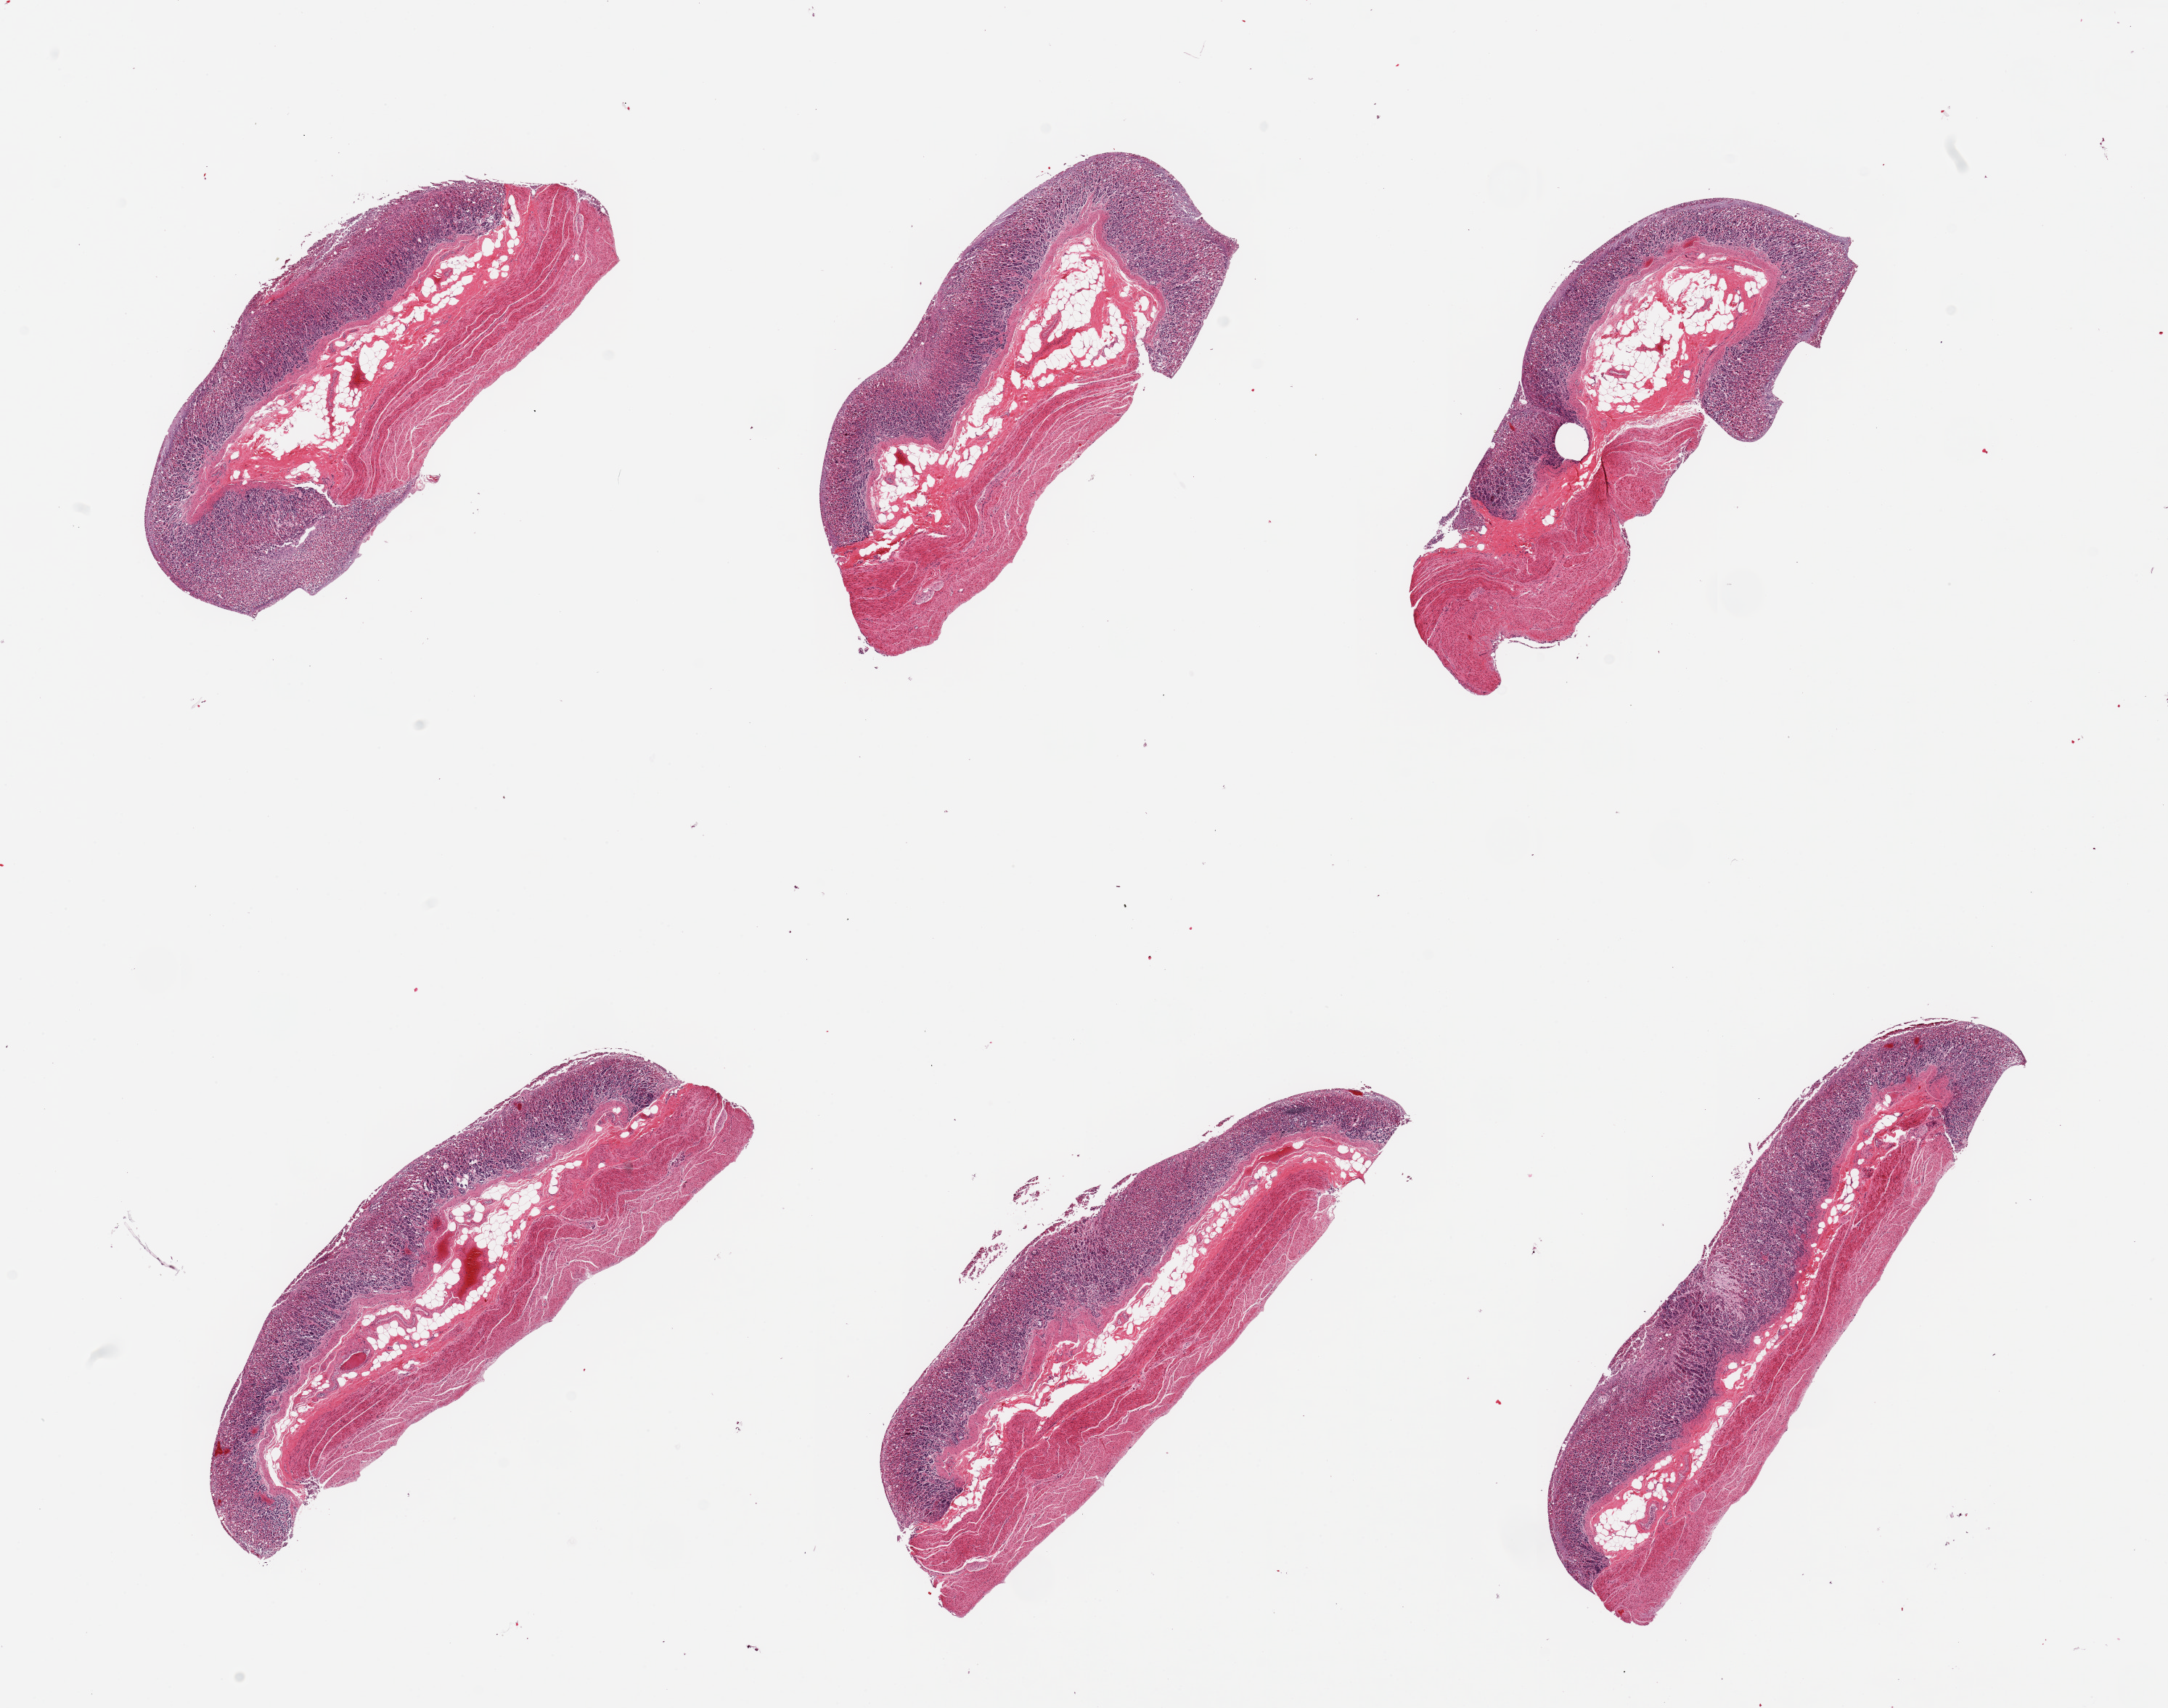
Digitized H&E-stained section, brightfield — low-resolution overview of the scanned area, about 23.6 x 18.6 mm, PAXgene-fixed, paraffin-embedded tissue, section of stomach (target tissue), tissue donor sample. Donor sex: male.
Reviewer comment on this tissue sample: 6 pieces; moderately autolyzed mucosa.